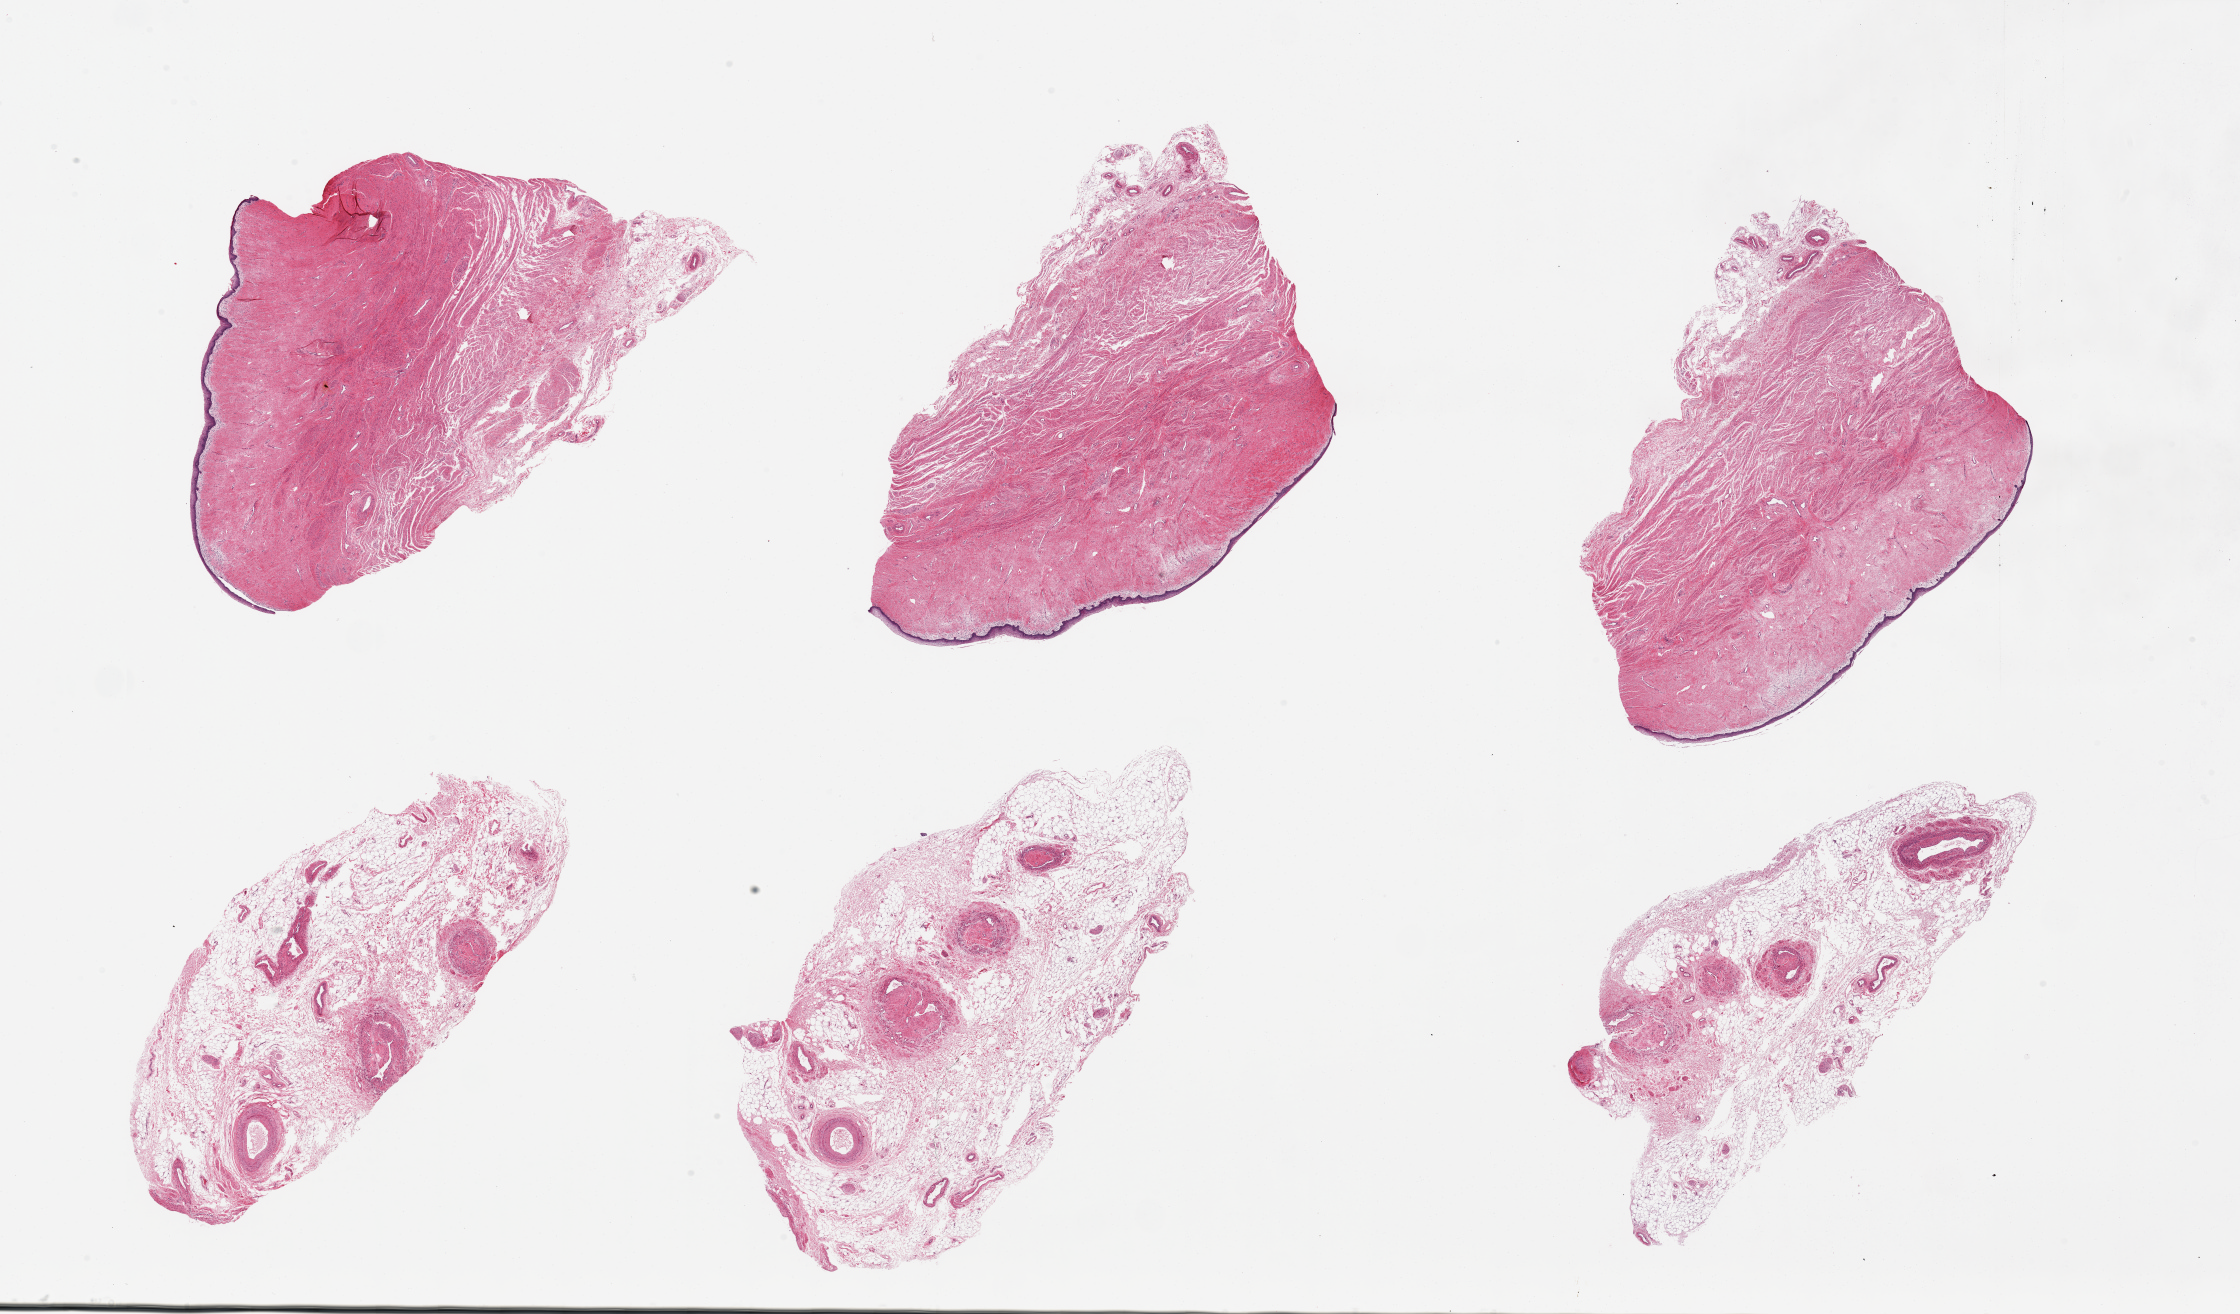
Digitized H&E-stained section, brightfield, a low-resolution overview of the entire scanned area, about 35.4 x 20.8 mm (acquisition: 20x scan); PAXgene-fixed, paraffin-embedded tissue; section of vagina (target tissue); tissue donor sample. Donor: female.
Reviewer comment on this tissue sample: 6 pieces, up to 9.5x5.5mm; 3 have vagina, 3 have only fibrofatty tissue. The epithelium makes up only 2% of the specimen's thickness in most vaginal specimens (as in this one). The rest is fibromuscular stroma.